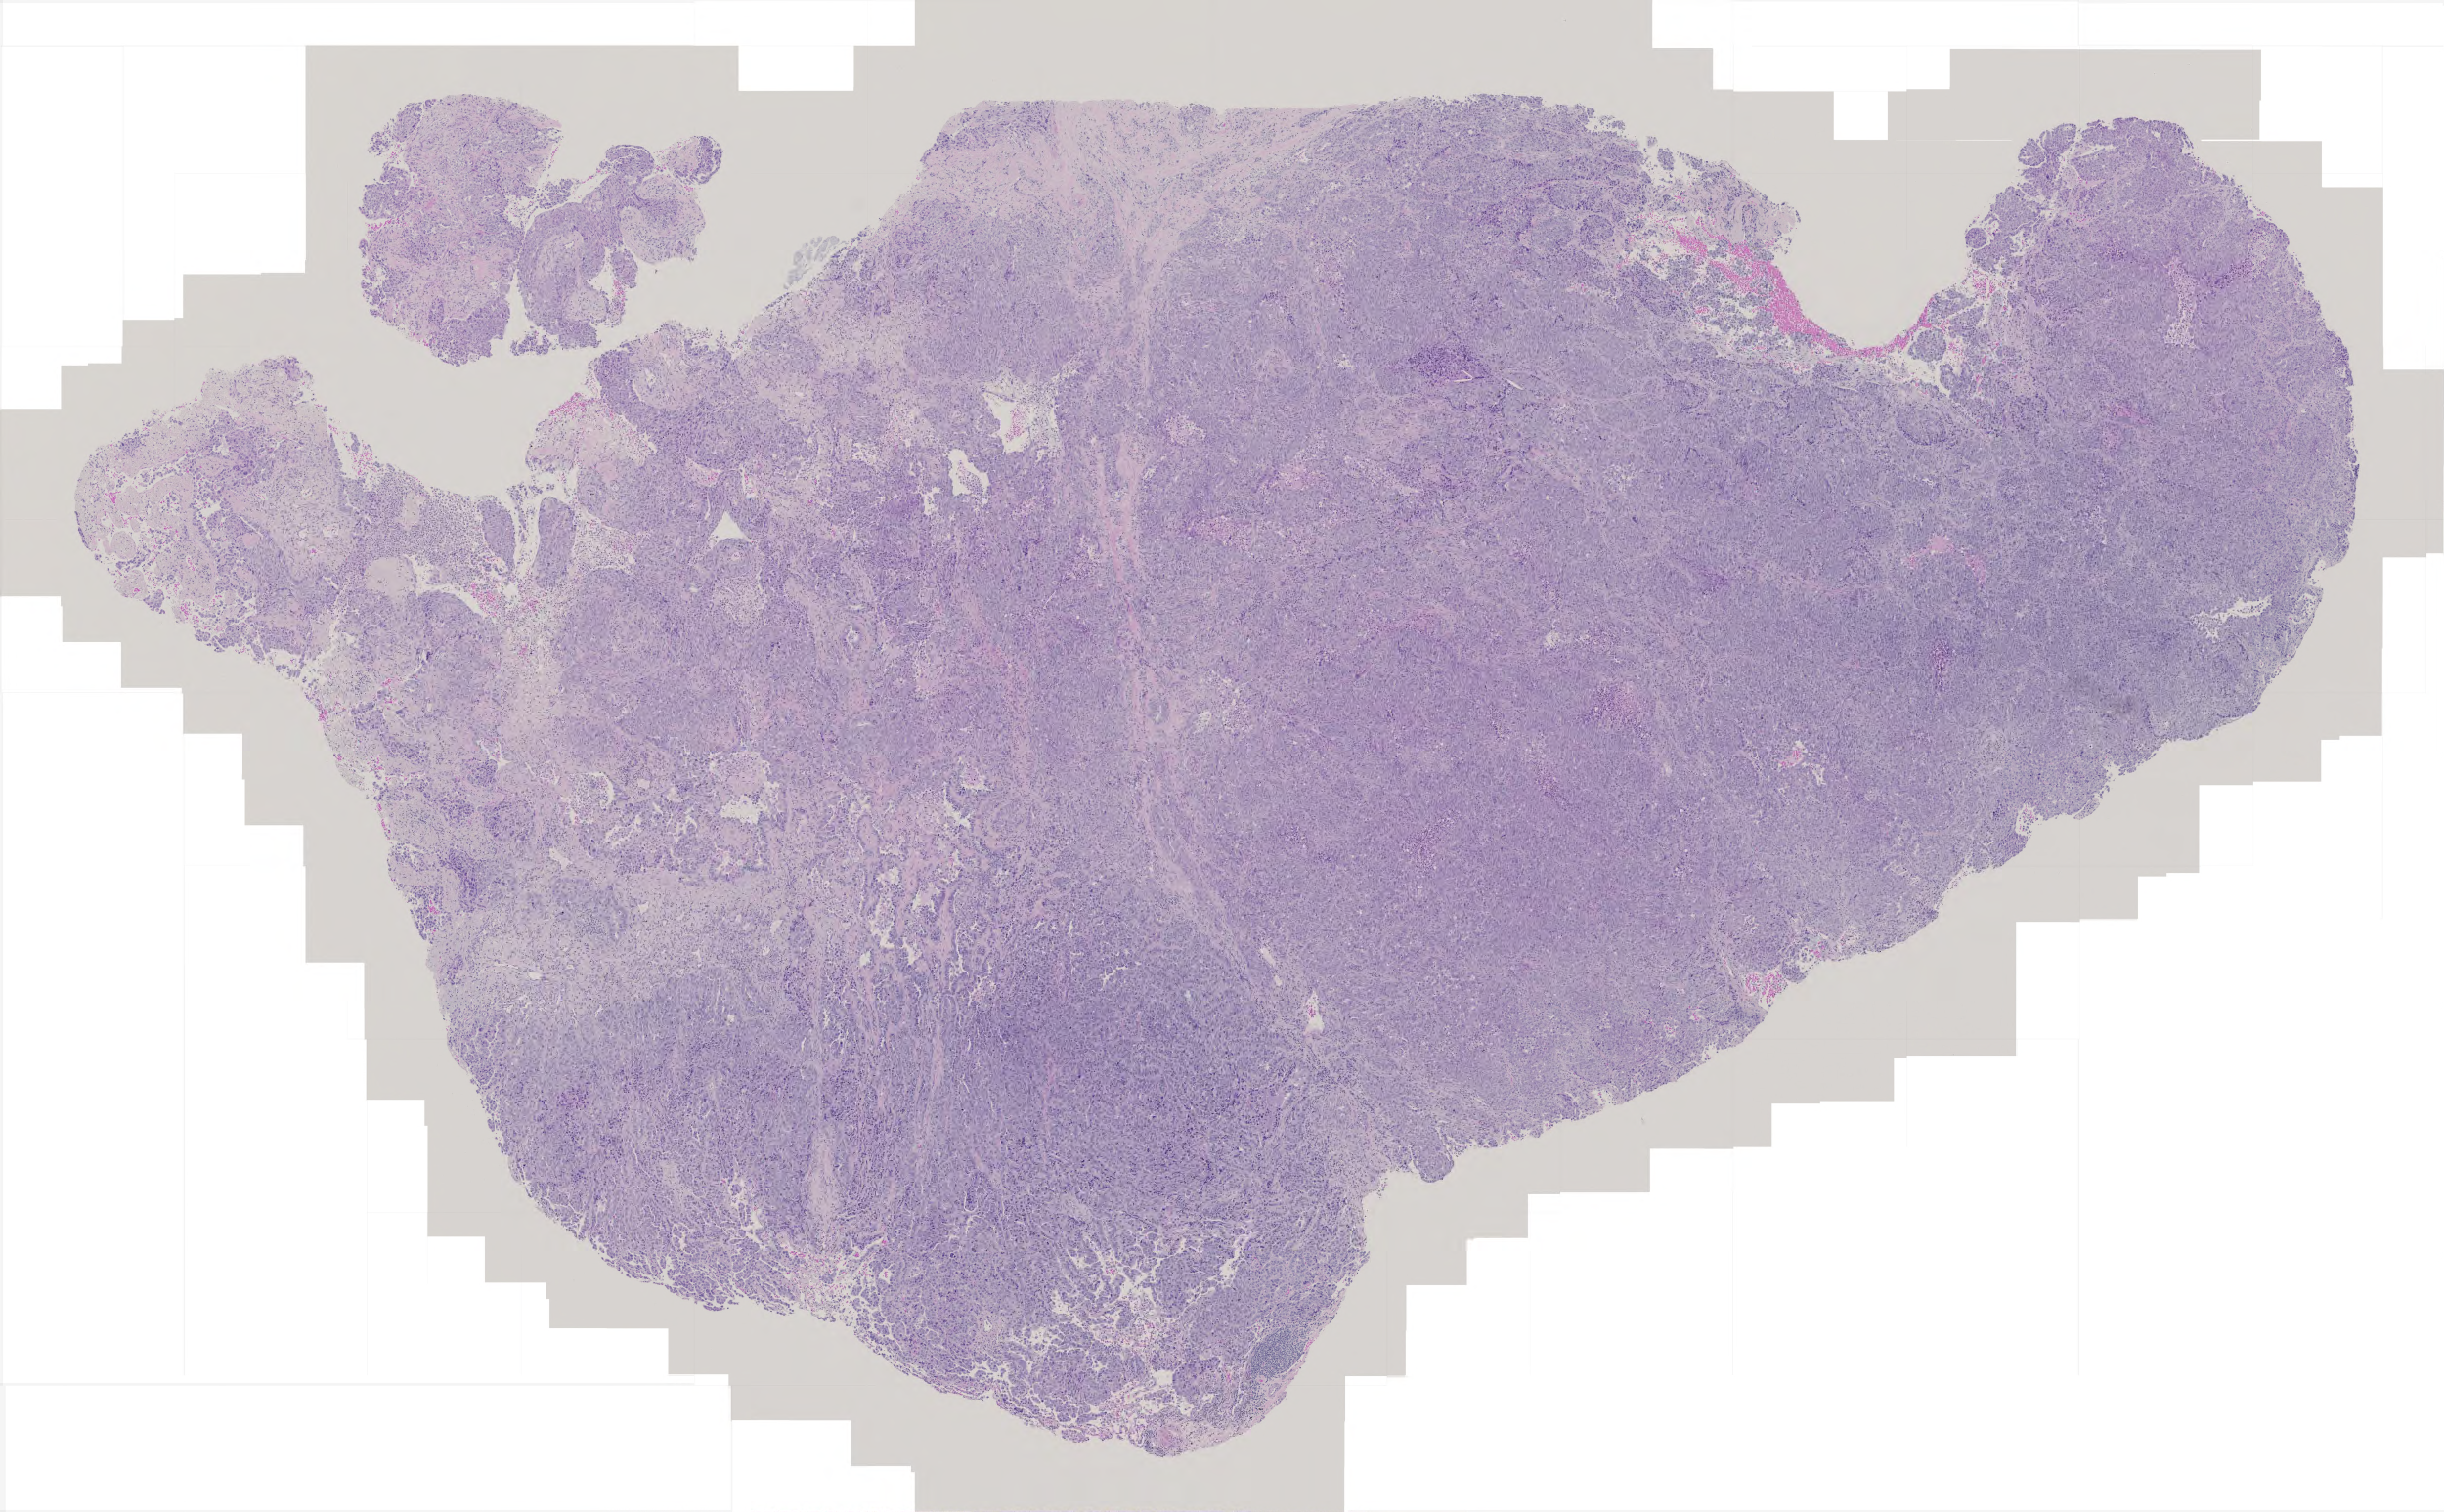
H&E whole-slide image, whole scanned area (about 5.0 x 3.1 mm) shown as a low-resolution overview. FFPE section. Lung, primary tumour sample. Patient: male, age at initial diagnosis 57 years.
* AJCC pathologic stage: IIA
* histologic diagnosis: Adenocarcinoma with mixed subtypes
* TNM: T1b N1 M0
* laterality: right